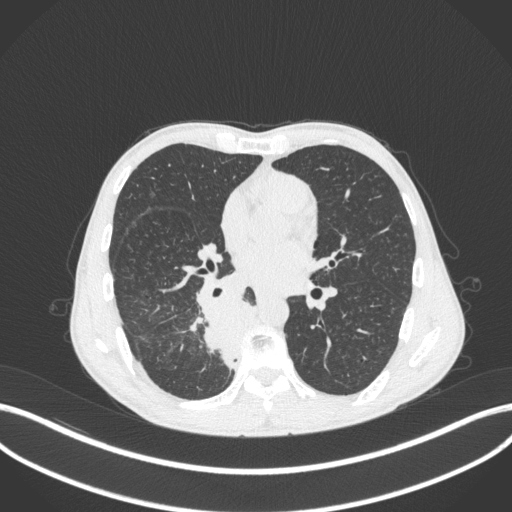
Chest CT, one axial slice. Slice 186 of 371 in the series (ordered by position). 120 kVp. Lung window (W 1500 / L -600 HU). 1 mm slice thickness. 512 × 512 image matrix, field of view 400 × 400 mm. Male patient, age 58 years. From the clinical record (not read from this slice): clinical TNM (as recorded): T3 N1 M1.
Outlined on this slice (rectangle marked by the reading radiologist):
- lung tumour (recorded histology: squamous cell carcinoma): bounding box (x1, y1, x2, y2) in pixels: (194, 299, 259, 366)